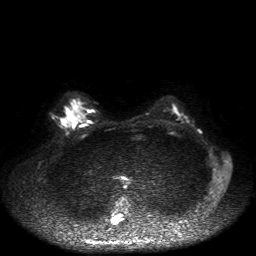
Breast MRI, one axial slice; slice 30 of 50 in the series (ordered by position); diffusion-weighted series; image 2 of 4 stored at this slice position (different b-values; order by instance number); 1.5 T; 4 mm slice thickness; 256 × 256 image matrix, field of view 360 × 360 mm. Female patient.
Outlined on this slice (expert manual segmentation):
- tumour on diffusion-weighted imaging: bounding box (x1, y1, x2, y2) in pixels: (62, 119, 66, 124)